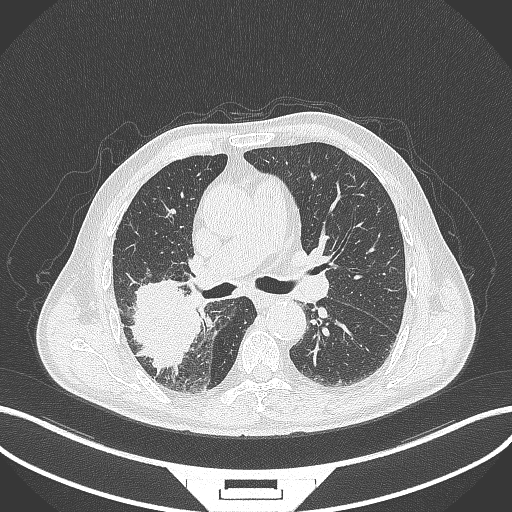
Chest CT, one axial slice. Slice 243 of 429 in the series (ordered by position). Reconstruction kernel B70f. 120 kVp. Lung window (W 1500 / L -600 HU). 1 mm slice thickness. 512 × 512 image matrix, field of view 400 × 400 mm. Patient: male, 72 years. Case-level facts recorded for this patient, not image findings: clinical TNM (as recorded): T3 N2 M0.
Outlined on this slice (rectangle marked by the reading radiologist):
- lung tumour (recorded histology: adenocarcinoma): bounding box [x1, y1, x2, y2] px = [124, 277, 204, 374]